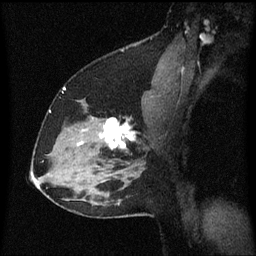
Breast MRI (dynamic contrast-enhanced), one sagittal slice; position 42 of 60 along the scan axis; dynamic contrast-enhanced series, image 2 of 3 at this slice position (ordered by acquisition); 1.5 T; TE 4.2 ms, TR 8.4 ms; 2 mm slice thickness; 256 × 256 image matrix, field of view 200 × 200 mm. Female patient, age 37 years. From the clinical record (not read from this slice): setting: breast cancer imaged before/during neoadjuvant chemotherapy; receptor status: HR-positive, HER2-negative.
Structures marked on this image (semi-automatically segmented with operator editing):
- analysis volume of interest (the breast-tissue region the enhancement analysis was run in; not a lesion): box from (x=94, y=118) to (x=141, y=157) px
- tumour enhancement mask (voxels above the 70 % enhancement threshold inside the analysis volume of interest): (x=102, y=118)–(x=135, y=149)